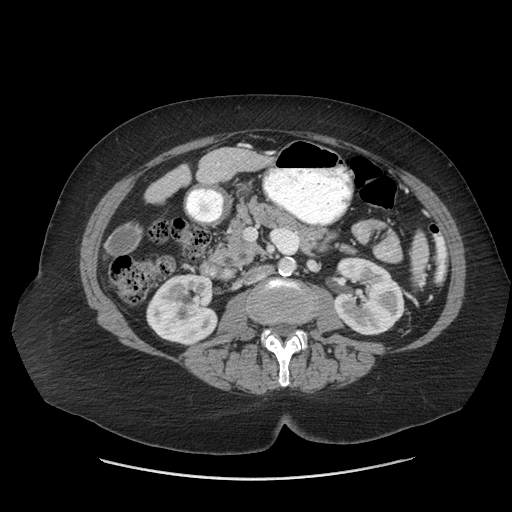
Contrast-enhanced abdominal CT (liver protocol), one axial slice. Reconstruction kernel STANDARD. Soft-tissue window (W 400 / L 40 HU). 2.5 mm slice thickness. 512 × 512 image matrix. Case-level facts recorded for this patient, not image findings: diagnosis: hepatocellular carcinoma (patient treated with transarterial chemoembolisation; whether this scan precedes or follows treatment is not stated here); TNM stage (as recorded): Stage-IIIB; Child-Pugh class: A.
Annotated regions visible in this slice (semi-automatic segmentation, software-assisted and operator-edited):
- liver parenchyma outside the tumour (the mass and vessels are separate outlines, so this box may not span the whole liver): box from (x=196, y=148) to (x=271, y=184) px
- liver vessels: (x=217, y=163)–(x=219, y=165)